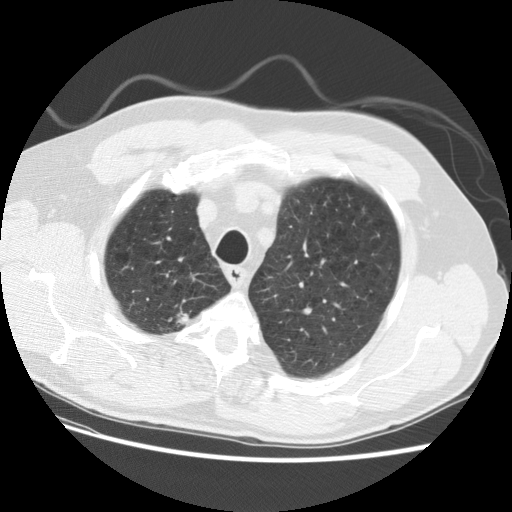
Low-dose screening chest CT, axial slice. Baseline annual screen. Lung window (W 1500 / L -600 HU). Standard (soft-tissue) reconstruction kernel (STANDARD). Male, age 69 years at enrolment. Former smoker at enrolment.
Expert reader's lesion annotation, bounding box (x1, y1, x2, y2) in pixels: (159, 304, 201, 334). Reader record for this screening exam (exam-level; its link to the box is not recorded): non-calcified nodule or mass ≥4 mm, right upper lobe, 15 × 15 mm, spiculated (stellate) margins, soft tissue attenuation. Official screen result: positive, change unspecified: nodule(s) >= 4 mm or enlarging nodule(s), mass(es), or other non-specific abnormalities suspicious for lung cancer. Lung cancer was diagnosed 22 days after this screen: large cell neuroendocrine carcinoma, right upper lobe, poorly differentiated (G3), stage IA (AJCC 6th edition), 23 mm at pathology.